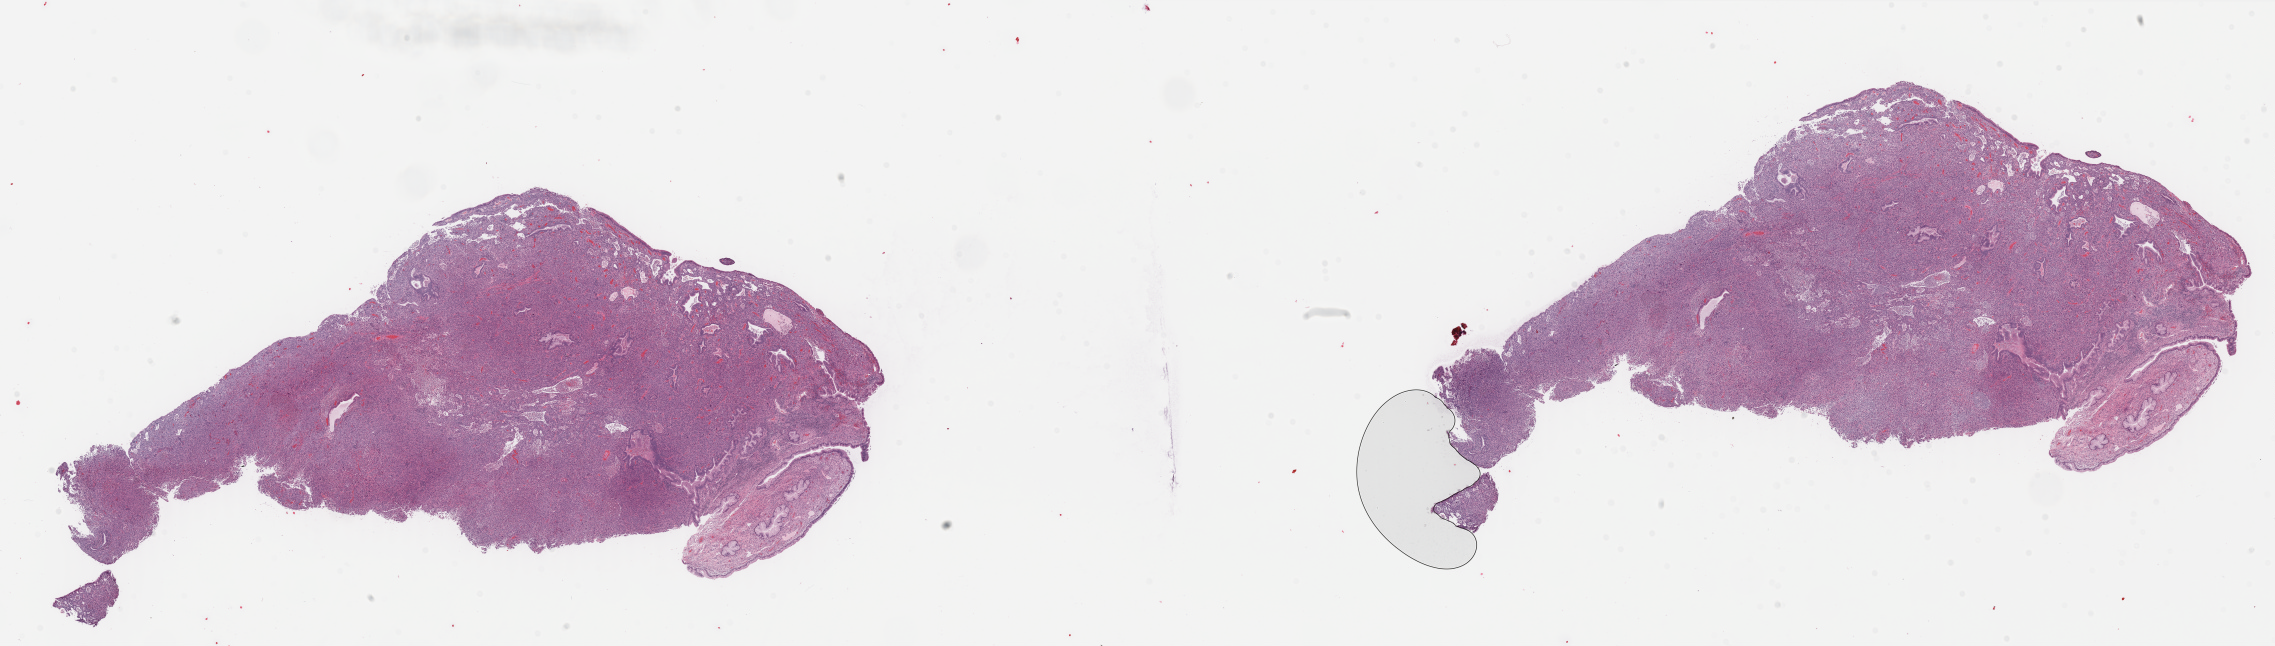
Whole-slide histology image, H&E, whole scanned area (about 36.0 x 10.2 mm, acquisition: 40x scan) shown as a low-resolution overview. Formalin-fixed paraffin-embedded (FFPE) diagnostic section. Primary tumour sample from the cervix. Female, age 32 years at initial diagnosis. Histologic grade: G3 (poorly differentiated).
Lymph nodes positive (case pathology): 0 of 22 examined. FIGO stage: IIA1. Pathologic diagnosis: Squamous cell carcinoma, NOS (cervix uteri).